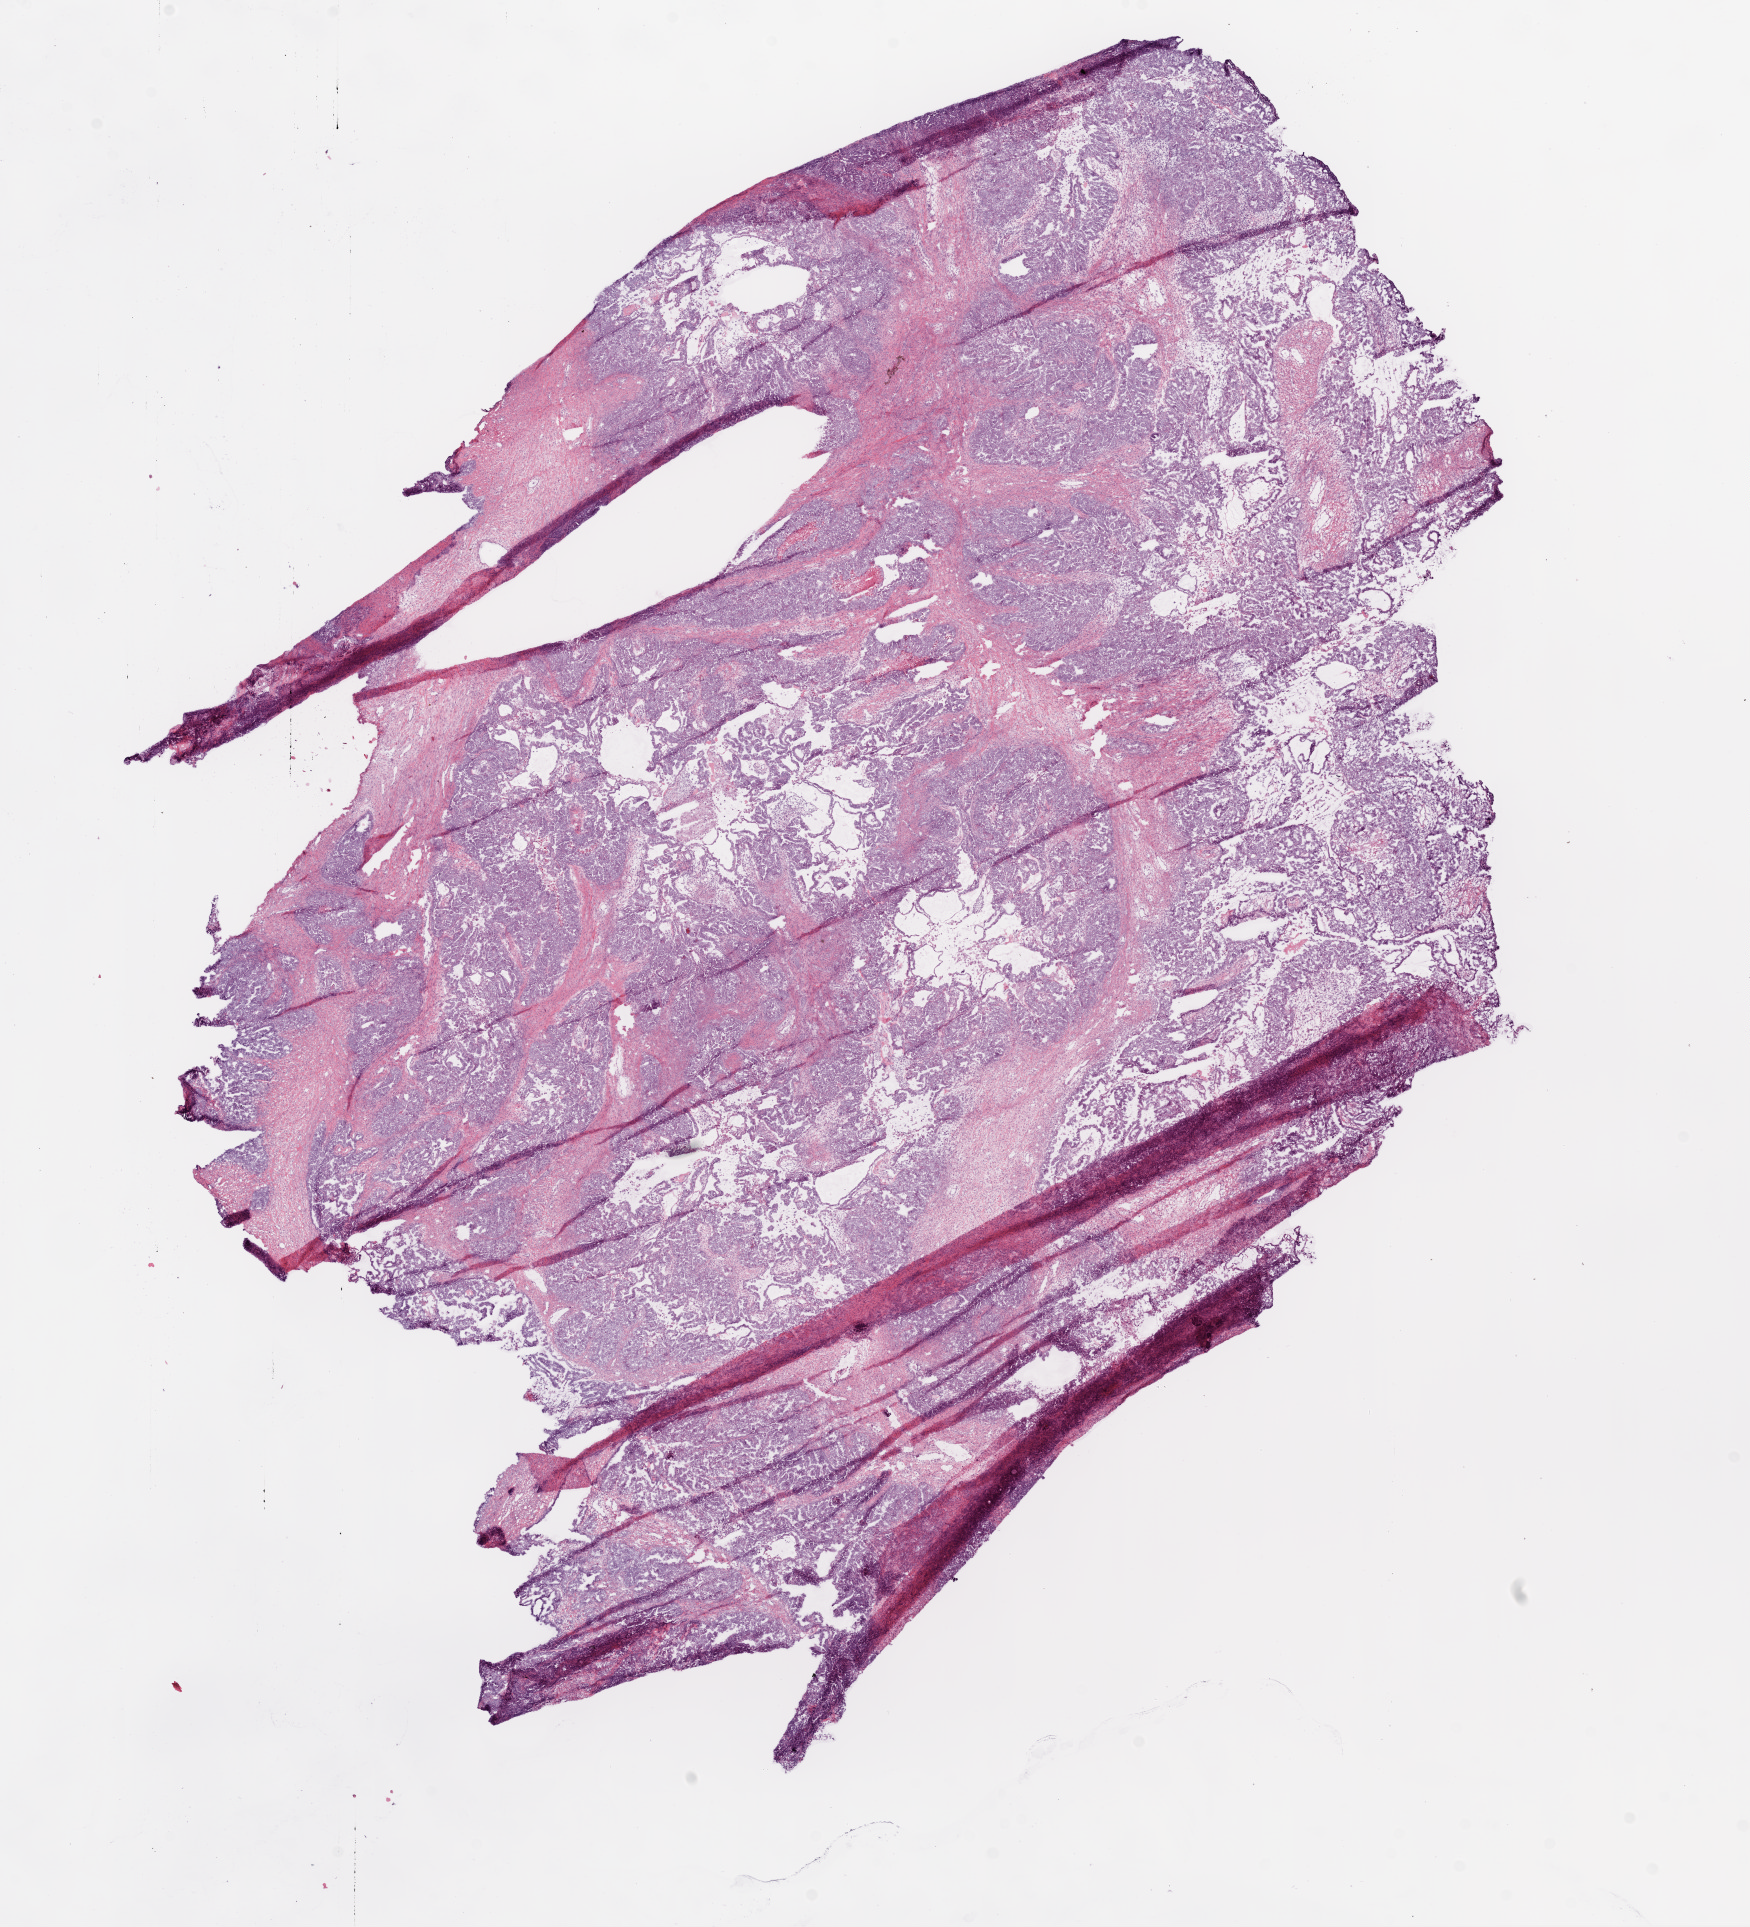
Digitized Hematoxylin and eosin (H&E) stained tissue section (whole slide), shown as a low-resolution overview of the whole scanned area (about 14.0 x 15.5 mm, acquisition: 20x scan); frozen section from the bottom of the tissue portion; primary tumour sample from the ovary. Female, age 78 years at initial diagnosis. Histologic grade: G3 (poorly differentiated). Pathologist review of this section (percent, as recorded): tumour cells 85%, tumour nuclei 90%, normal cells 0%, stromal cells 10%, necrosis 5%.
- histologic diagnosis: Serous cystadenocarcinoma, NOS
- FIGO stage: IIIC